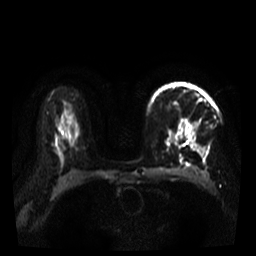
Breast MRI, one axial slice. Position 25 of 39 along the scan axis. Diffusion-weighted series; image 2 of 4 stored at this slice position (different b-values; order by instance number). 3 T. 5 mm slice thickness. 256 × 256 image matrix, field of view 320 × 320 mm. Female patient.
Outlined on this slice (outlined manually by an expert reader):
- tumour on diffusion-weighted imaging: bounding box (x1, y1, x2, y2) in pixels: (185, 124, 197, 140)